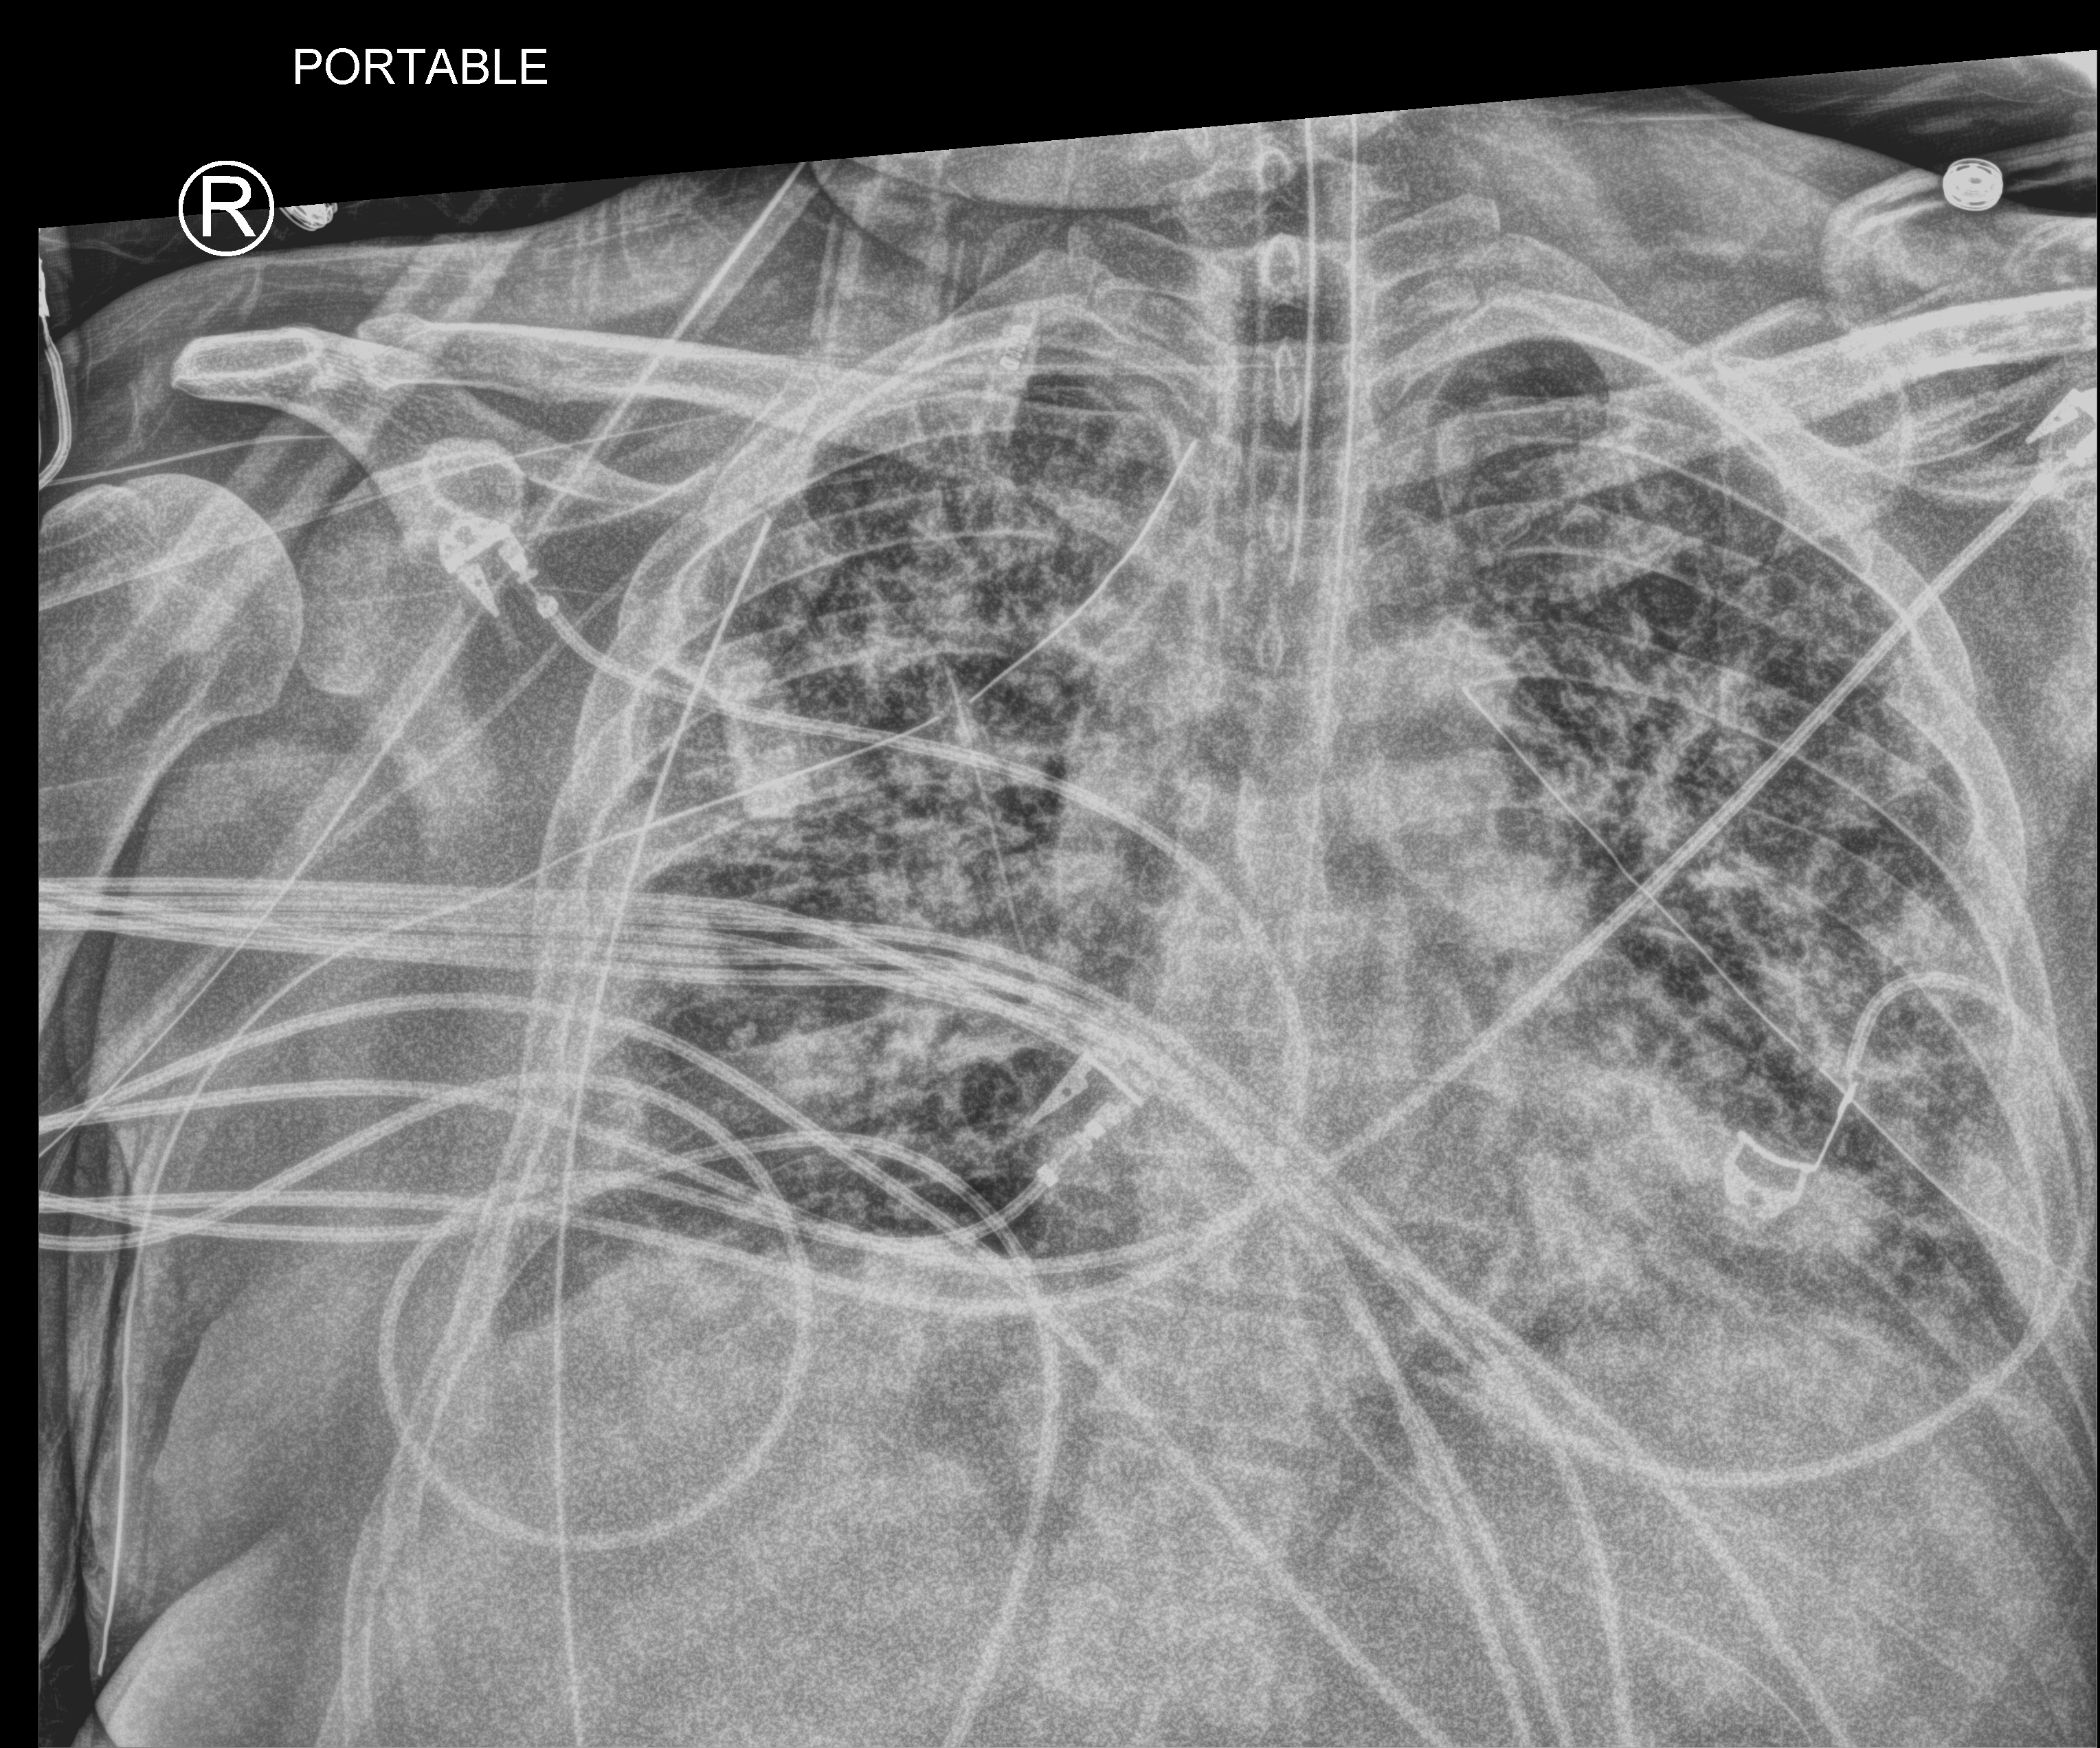
Chest X-ray (portable); anteroposterior (AP) projection. Patient hospitalised with COVID-19; male, aged 18–59 years.
From the hospital-stay record, not from the radiograph (when in the stay this image was taken is not recorded):
- mechanically ventilated during this hospital stay: yes
- admitted to intensive care during this hospital stay: yes